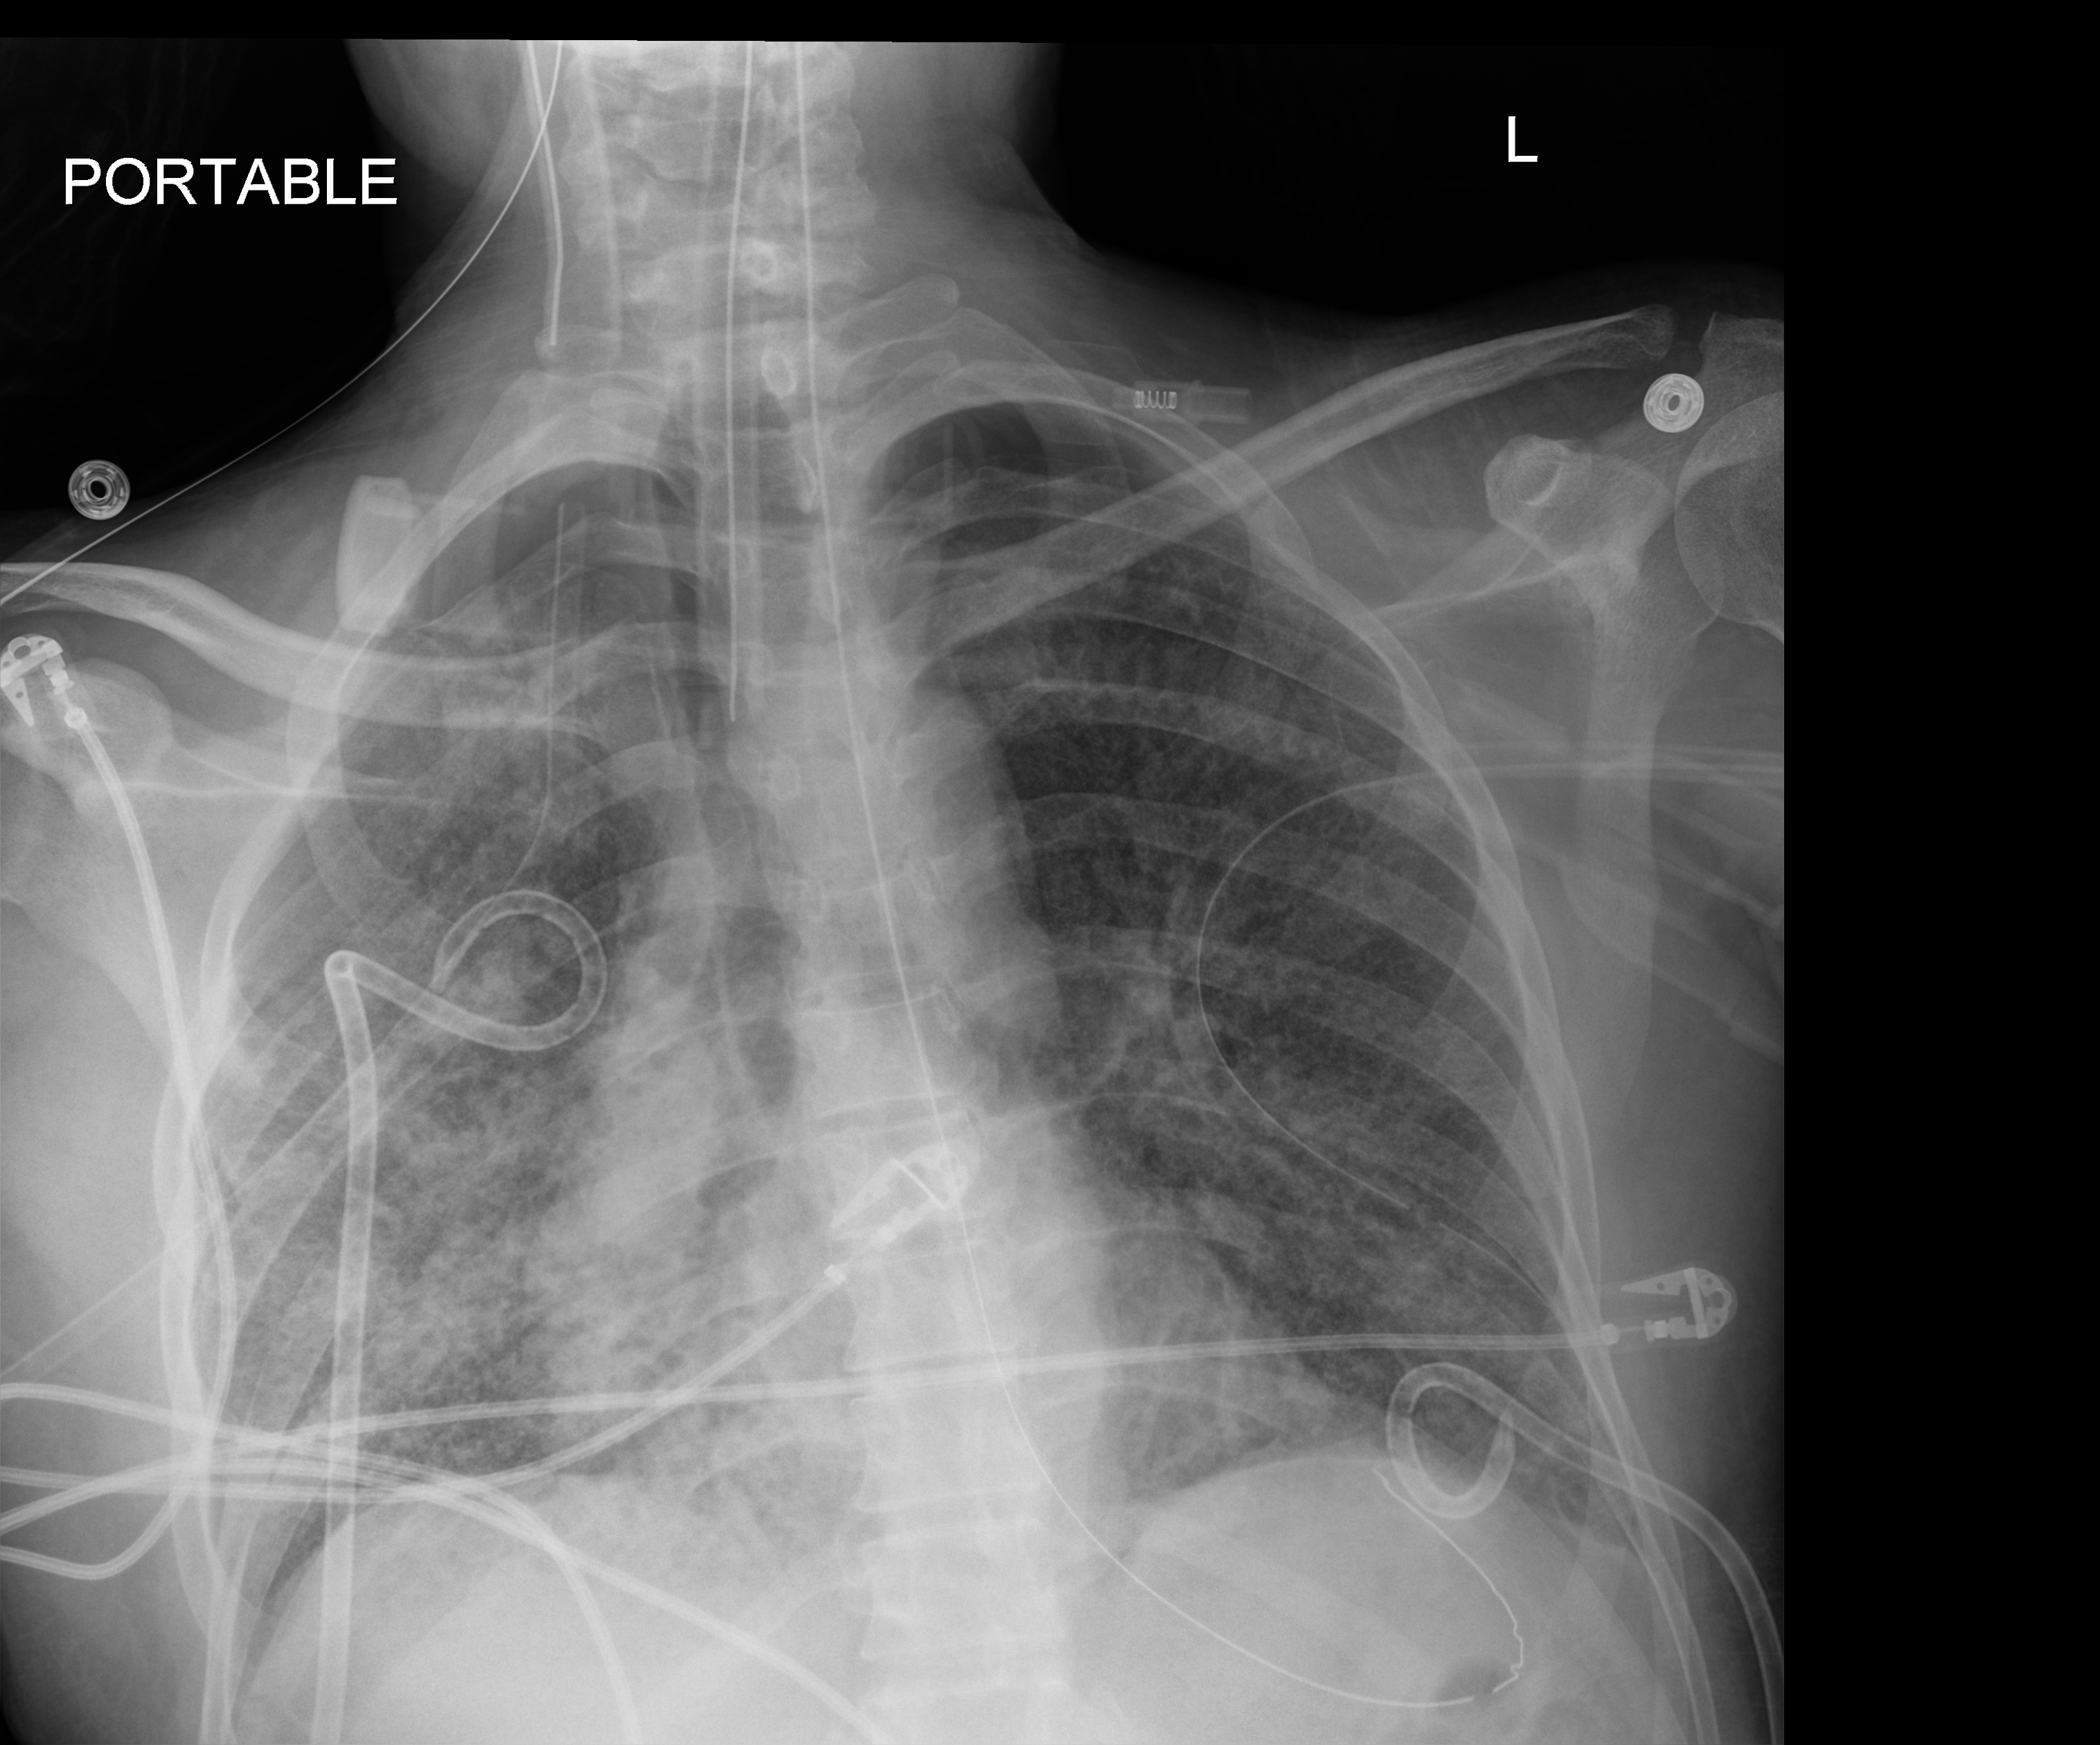
Bedside chest radiograph (digital radiography), anteroposterior (AP) projection. Adult patient hospitalised with COVID-19, age 18–59 years.
From the hospital-stay record, not from the radiograph (when in the stay this image was taken is not recorded): admitted to intensive care during this hospital stay: yes; other chronic lung disease (admission record): no.